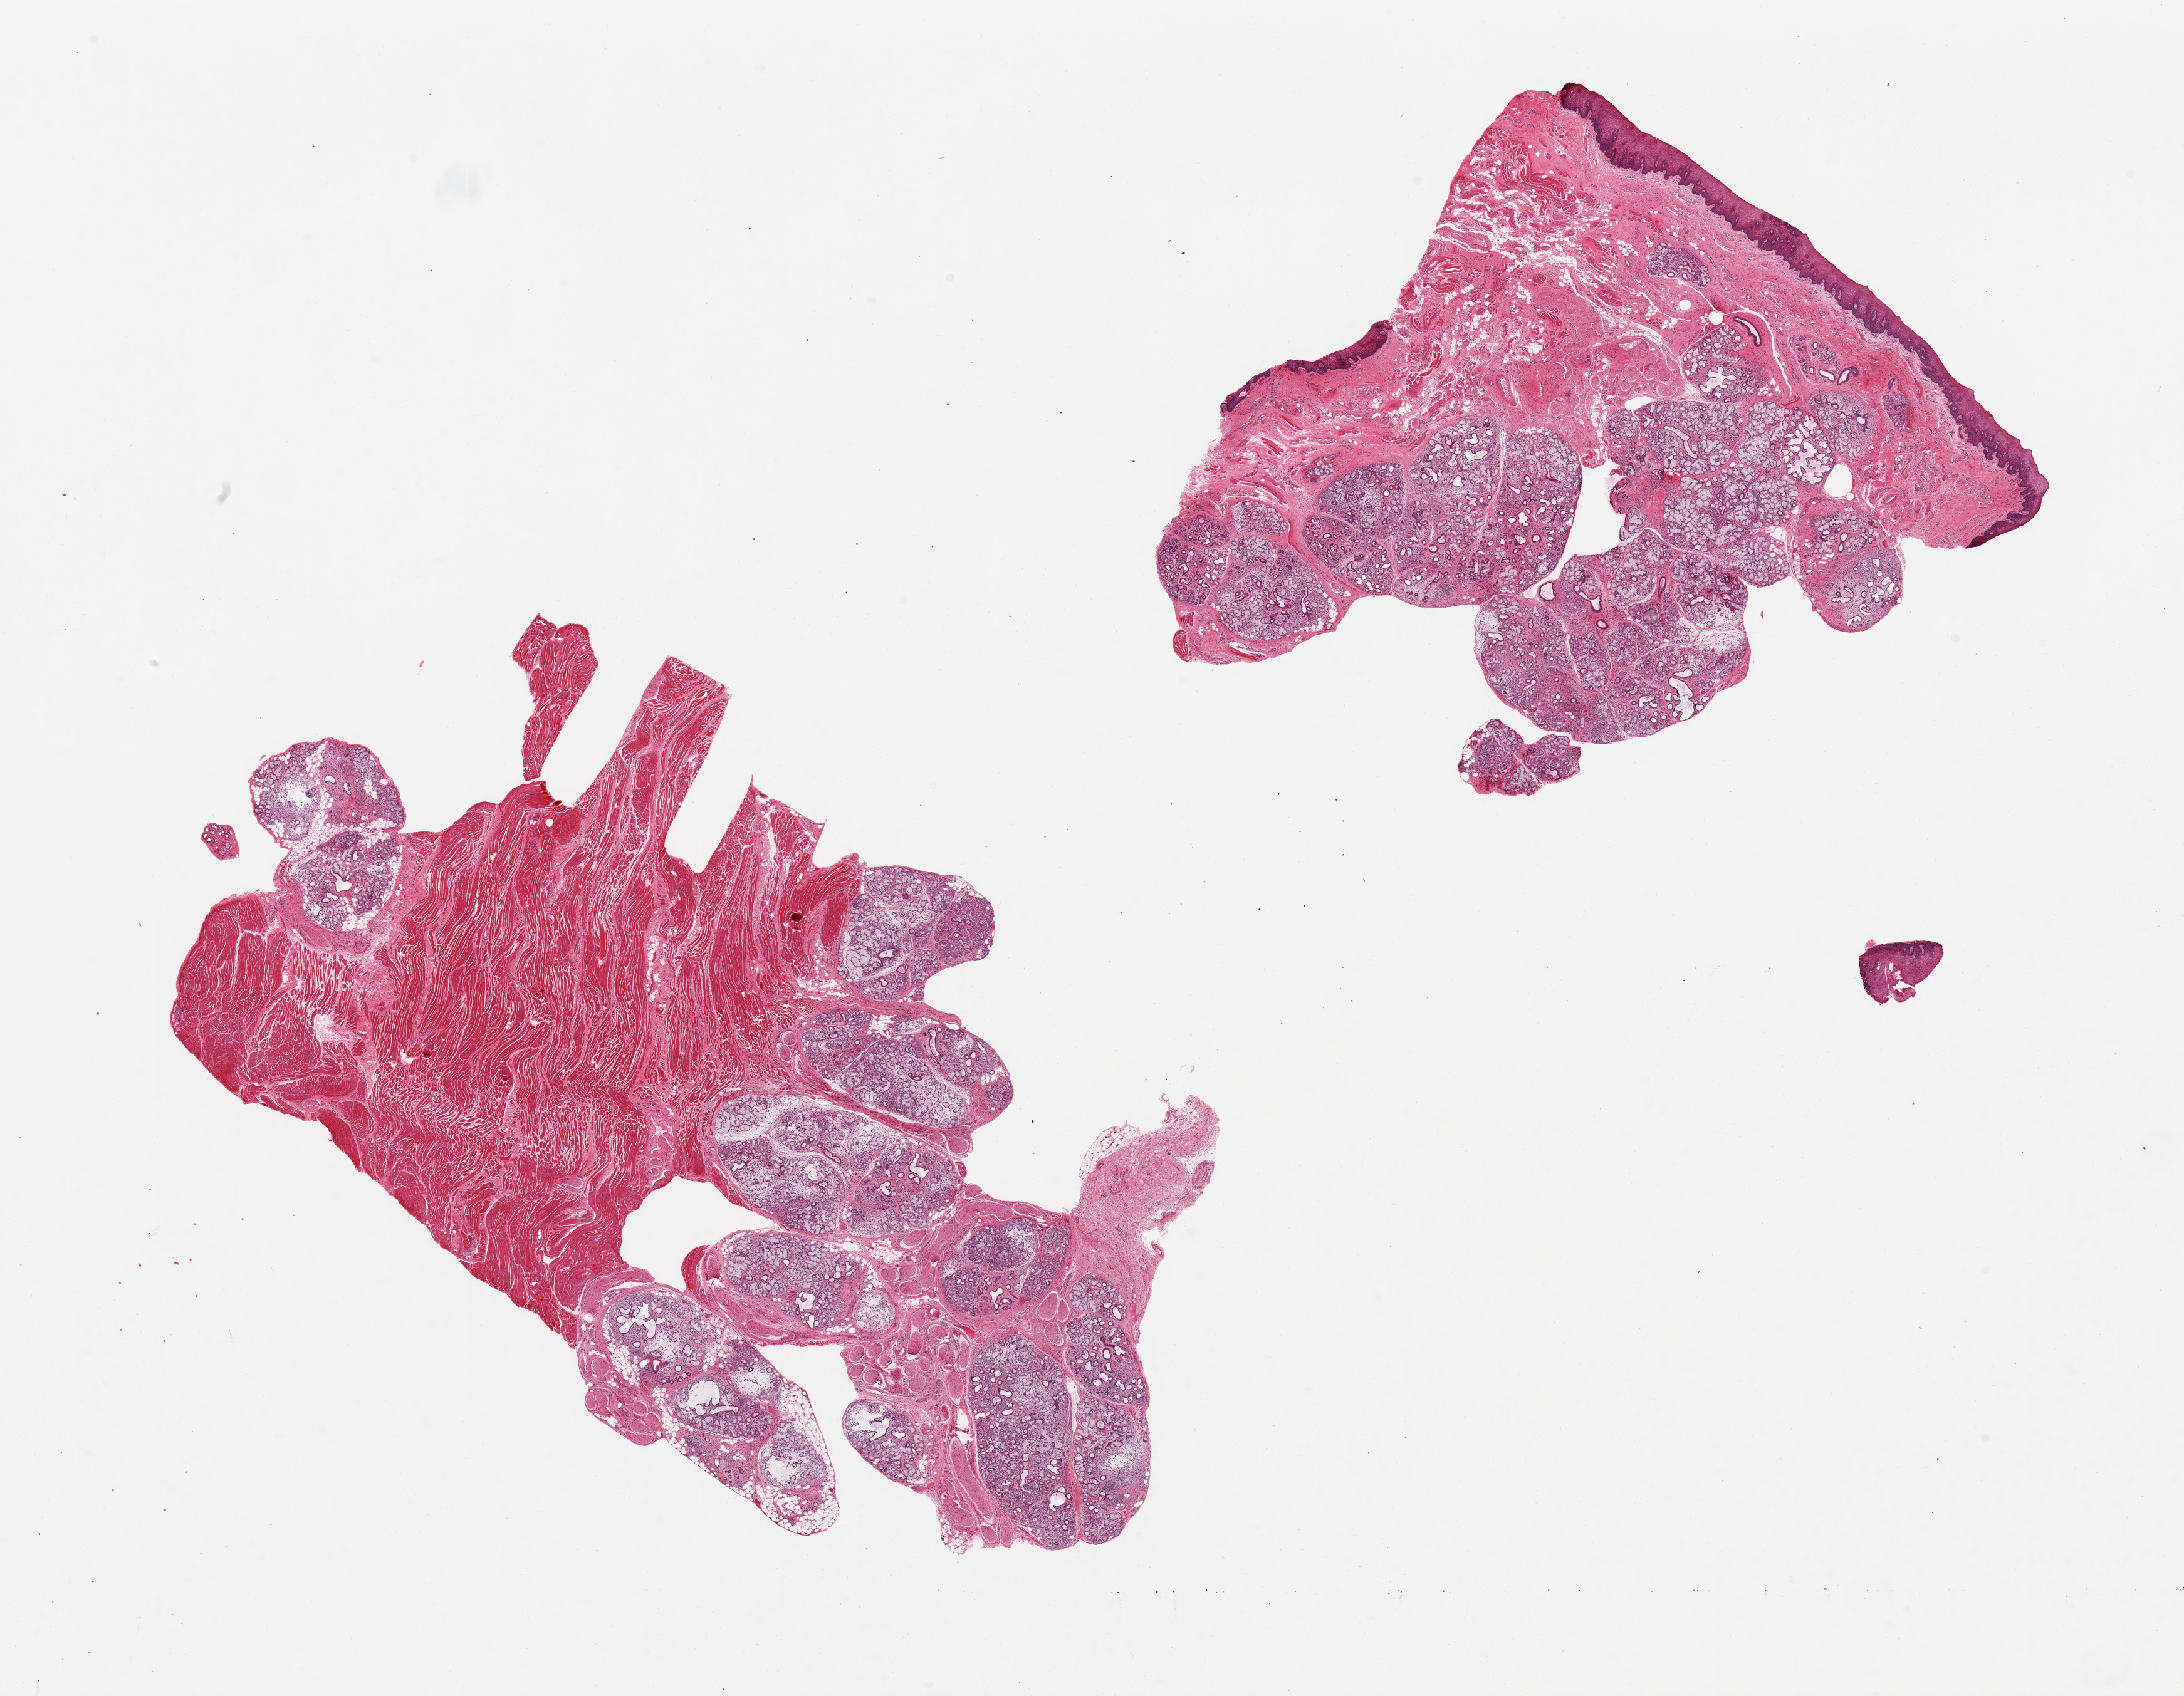
H&E whole-slide image, brightfield — a low-resolution overview of the entire scanned area, about 27.6 x 21.4 mm; PAXgene-fixed, paraffin-embedded tissue; target tissue: minor salivary gland; tissue donor sample. Donor: female.
- review note (as recorded): 2 pieces, glandular parenchyma is ~50% of each section; rest is skeletal muscae/squamous mucosa of lip